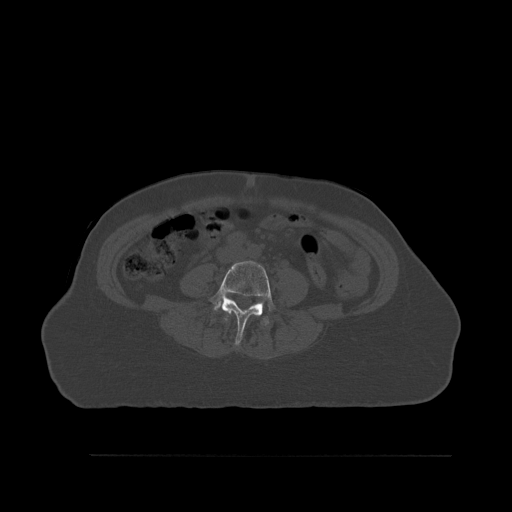
CT including the spine, one axial slice. Position 206 of 527 along the scan axis. Bone window (W 1800 / L 400 HU). 1.5 mm slice thickness. 512 × 512 image matrix. Female patient, age 73 years. From the clinical record (not read from this slice): primary cancer: breast.
Outlined on this slice (semi-automatically segmented with operator editing):
- L3 vertebra: bounding box <224,313,260,322> (left, top, right, bottom; pixels)
- L4 vertebra: <209,260,276,346>
- L5 vertebra: <213,302,269,325>